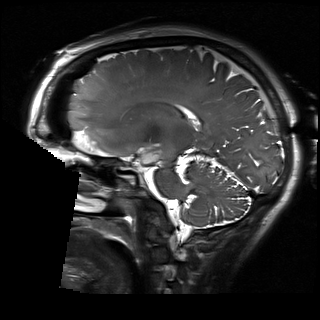
Brain MRI from a brain-tumour surgery series, one sagittal slice; slice 110 of 192 in the series (ordered by position); 1 mm slice thickness; 320 × 320 image matrix, field of view 230 × 230 mm. From the clinical record (not read from this slice): histopathology: Glioblastoma; WHO grade: 2; IDH mutation: no.
Outlined on this slice (outlined manually by an expert reader):
- residual tumour: bounding box (x1, y1, x2, y2) in pixels: (141, 151, 159, 164)